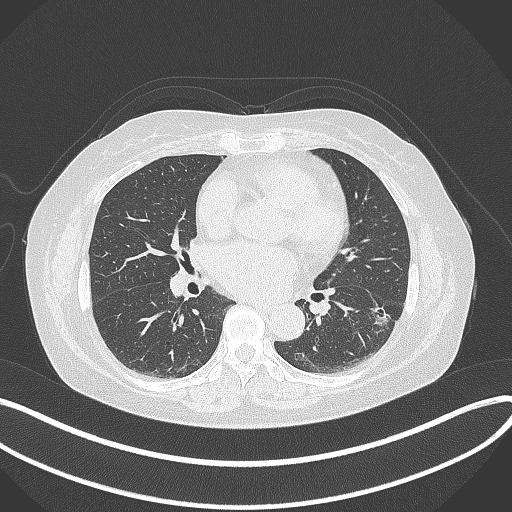
Chest CT, one axial slice; position 173 of 373 along the scan axis; lung window (W 1500 / L -600 HU); 1 mm slice thickness; 512 × 512 image matrix. Female patient, age 67 years. From the clinical record (not read from this slice): clinical TNM (as recorded): T1c N0 M0; histopathological grade: G2.
Structures marked on this image (rectangle marked by the reading radiologist):
- lung tumour (recorded histology: adenocarcinoma): bounding box (x1, y1, x2, y2) in pixels: (369, 301, 396, 334)